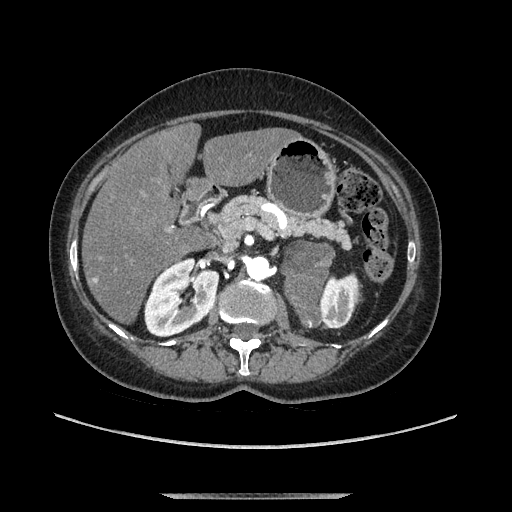
Contrast-enhanced abdominal CT, one axial slice; slice 63 of 169 in the series (ordered by position); soft-tissue window (W 400 / L 40 HU); 512 × 512 image matrix, field of view 400 × 400 mm. Female patient. Case-level facts recorded for this patient, not image findings: diagnosis: adrenocortical carcinoma; tumour side: left adrenal; tumour size at pathology: 9 cm; Ki-67 index: 2 %.
Structures marked on this image (semi-automatic segmentation, software-assisted and operator-edited):
- mass: bounding box [x1, y1, x2, y2] px = [285, 245, 331, 324]